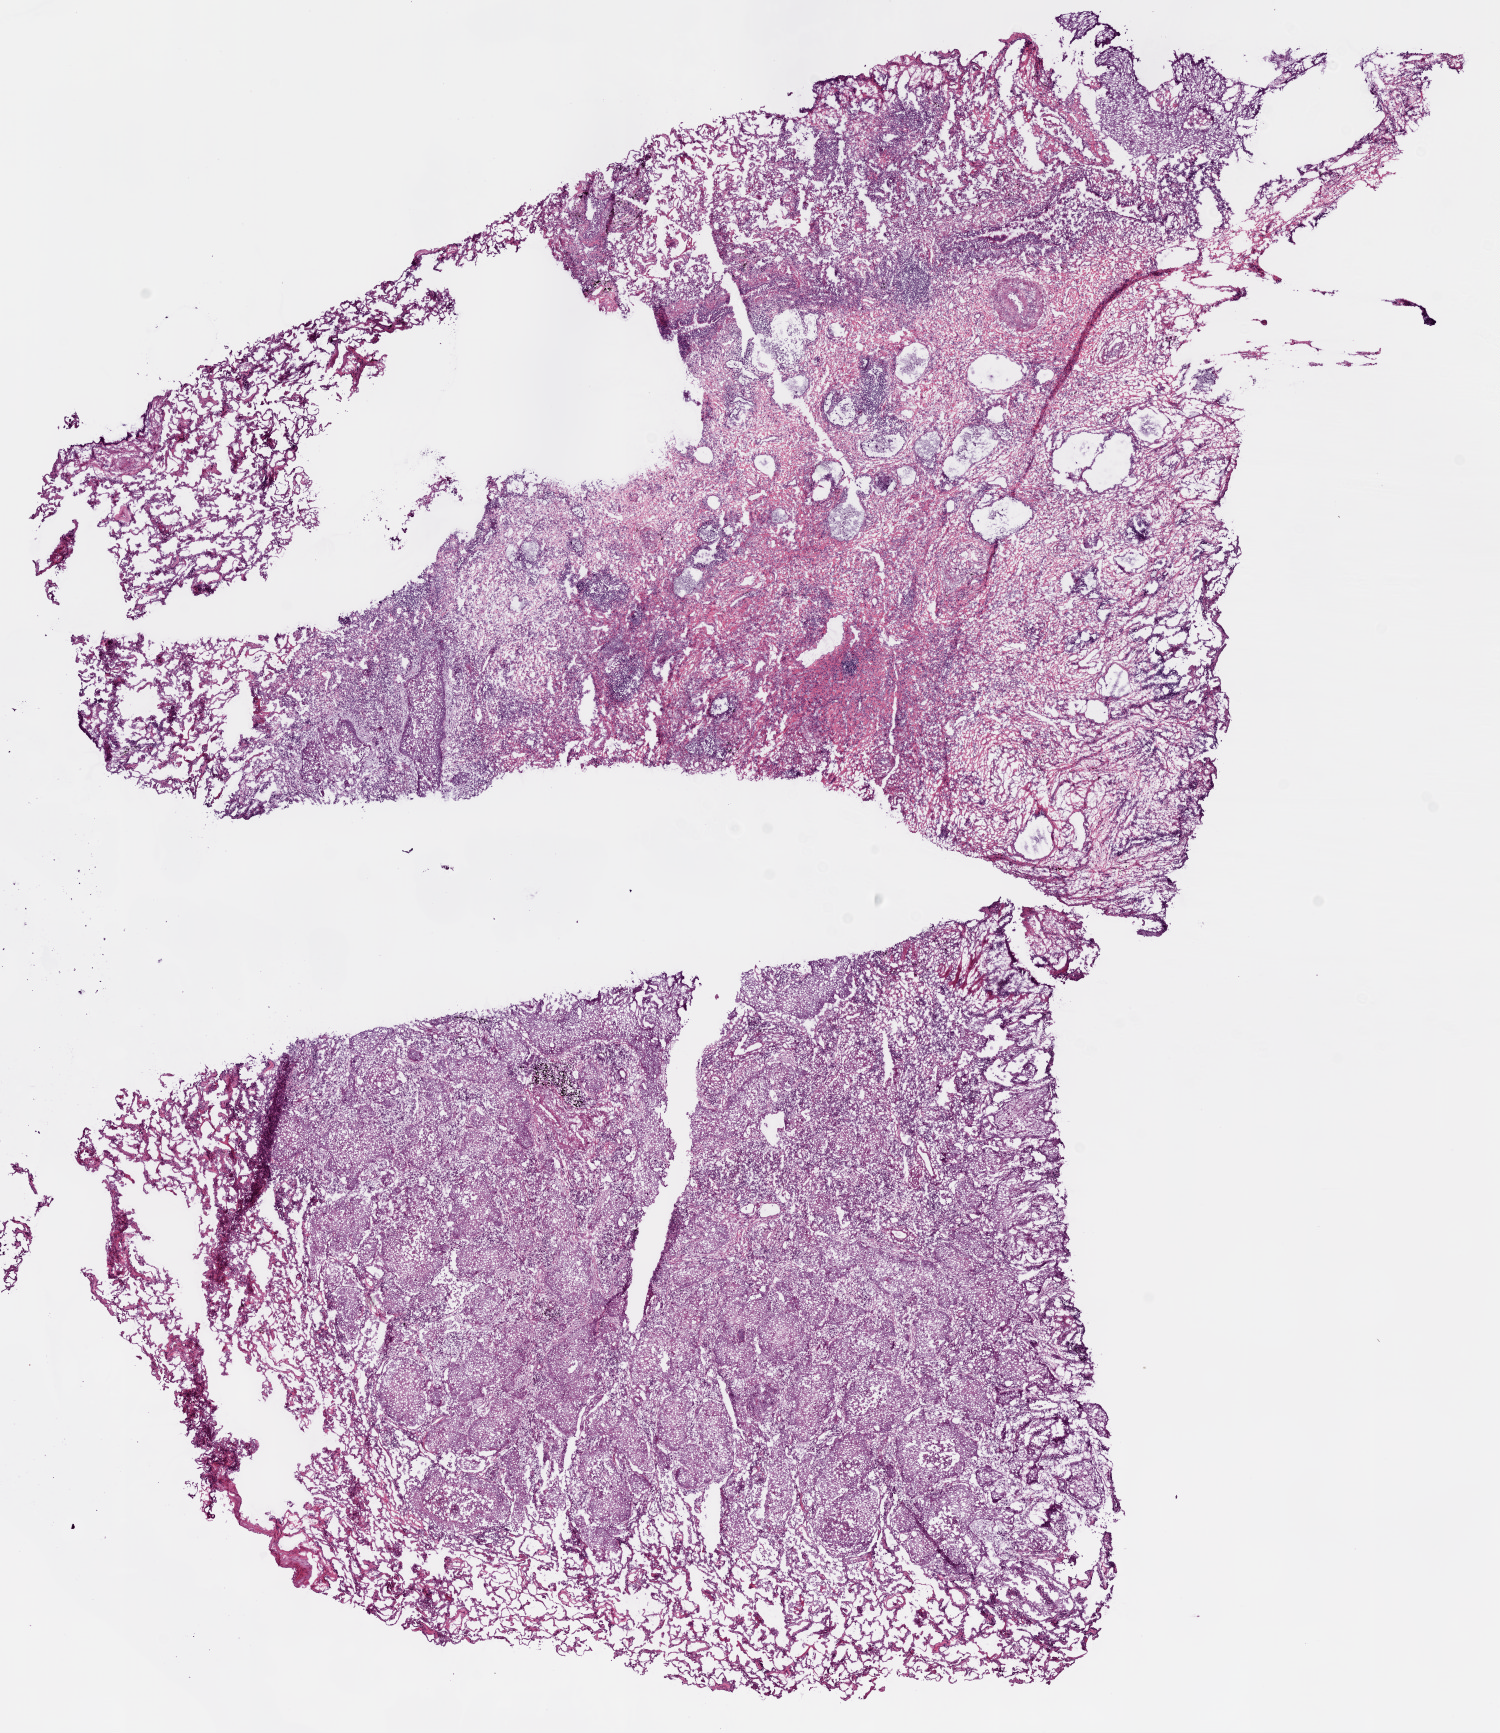
Whole-slide histology image, H&E — shown as a low-resolution overview of the whole scanned area (about 12.0 x 13.9 mm, from a 20x scan); frozen section; sample: primary tumour, lung. Female, age 80 years at initial diagnosis.
Pathologic diagnosis: Squamous cell carcinoma, NOS.